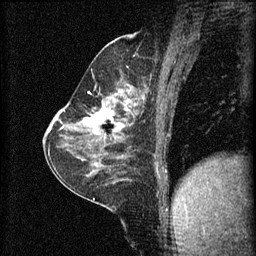
Breast MRI (dynamic contrast-enhanced), one sagittal slice; position 31 of 60 along the scan axis; 3 images stored at this slice position (order not interpretable as contrast timing); 1.5 T; TE 4.2 ms, TR 8.2 ms; 2 mm slice thickness; 256 × 256 image matrix. Patient: female, 59 years.
Structures marked on this image (semi-automatically segmented with operator editing):
- analysis volume of interest (the breast-tissue region the enhancement analysis was run in; not a lesion): bounding box <78,92,137,135> (left, top, right, bottom; pixels)
- tumour enhancement mask (voxels above the 70 % enhancement threshold inside the analysis volume of interest): <82,100,131,131>